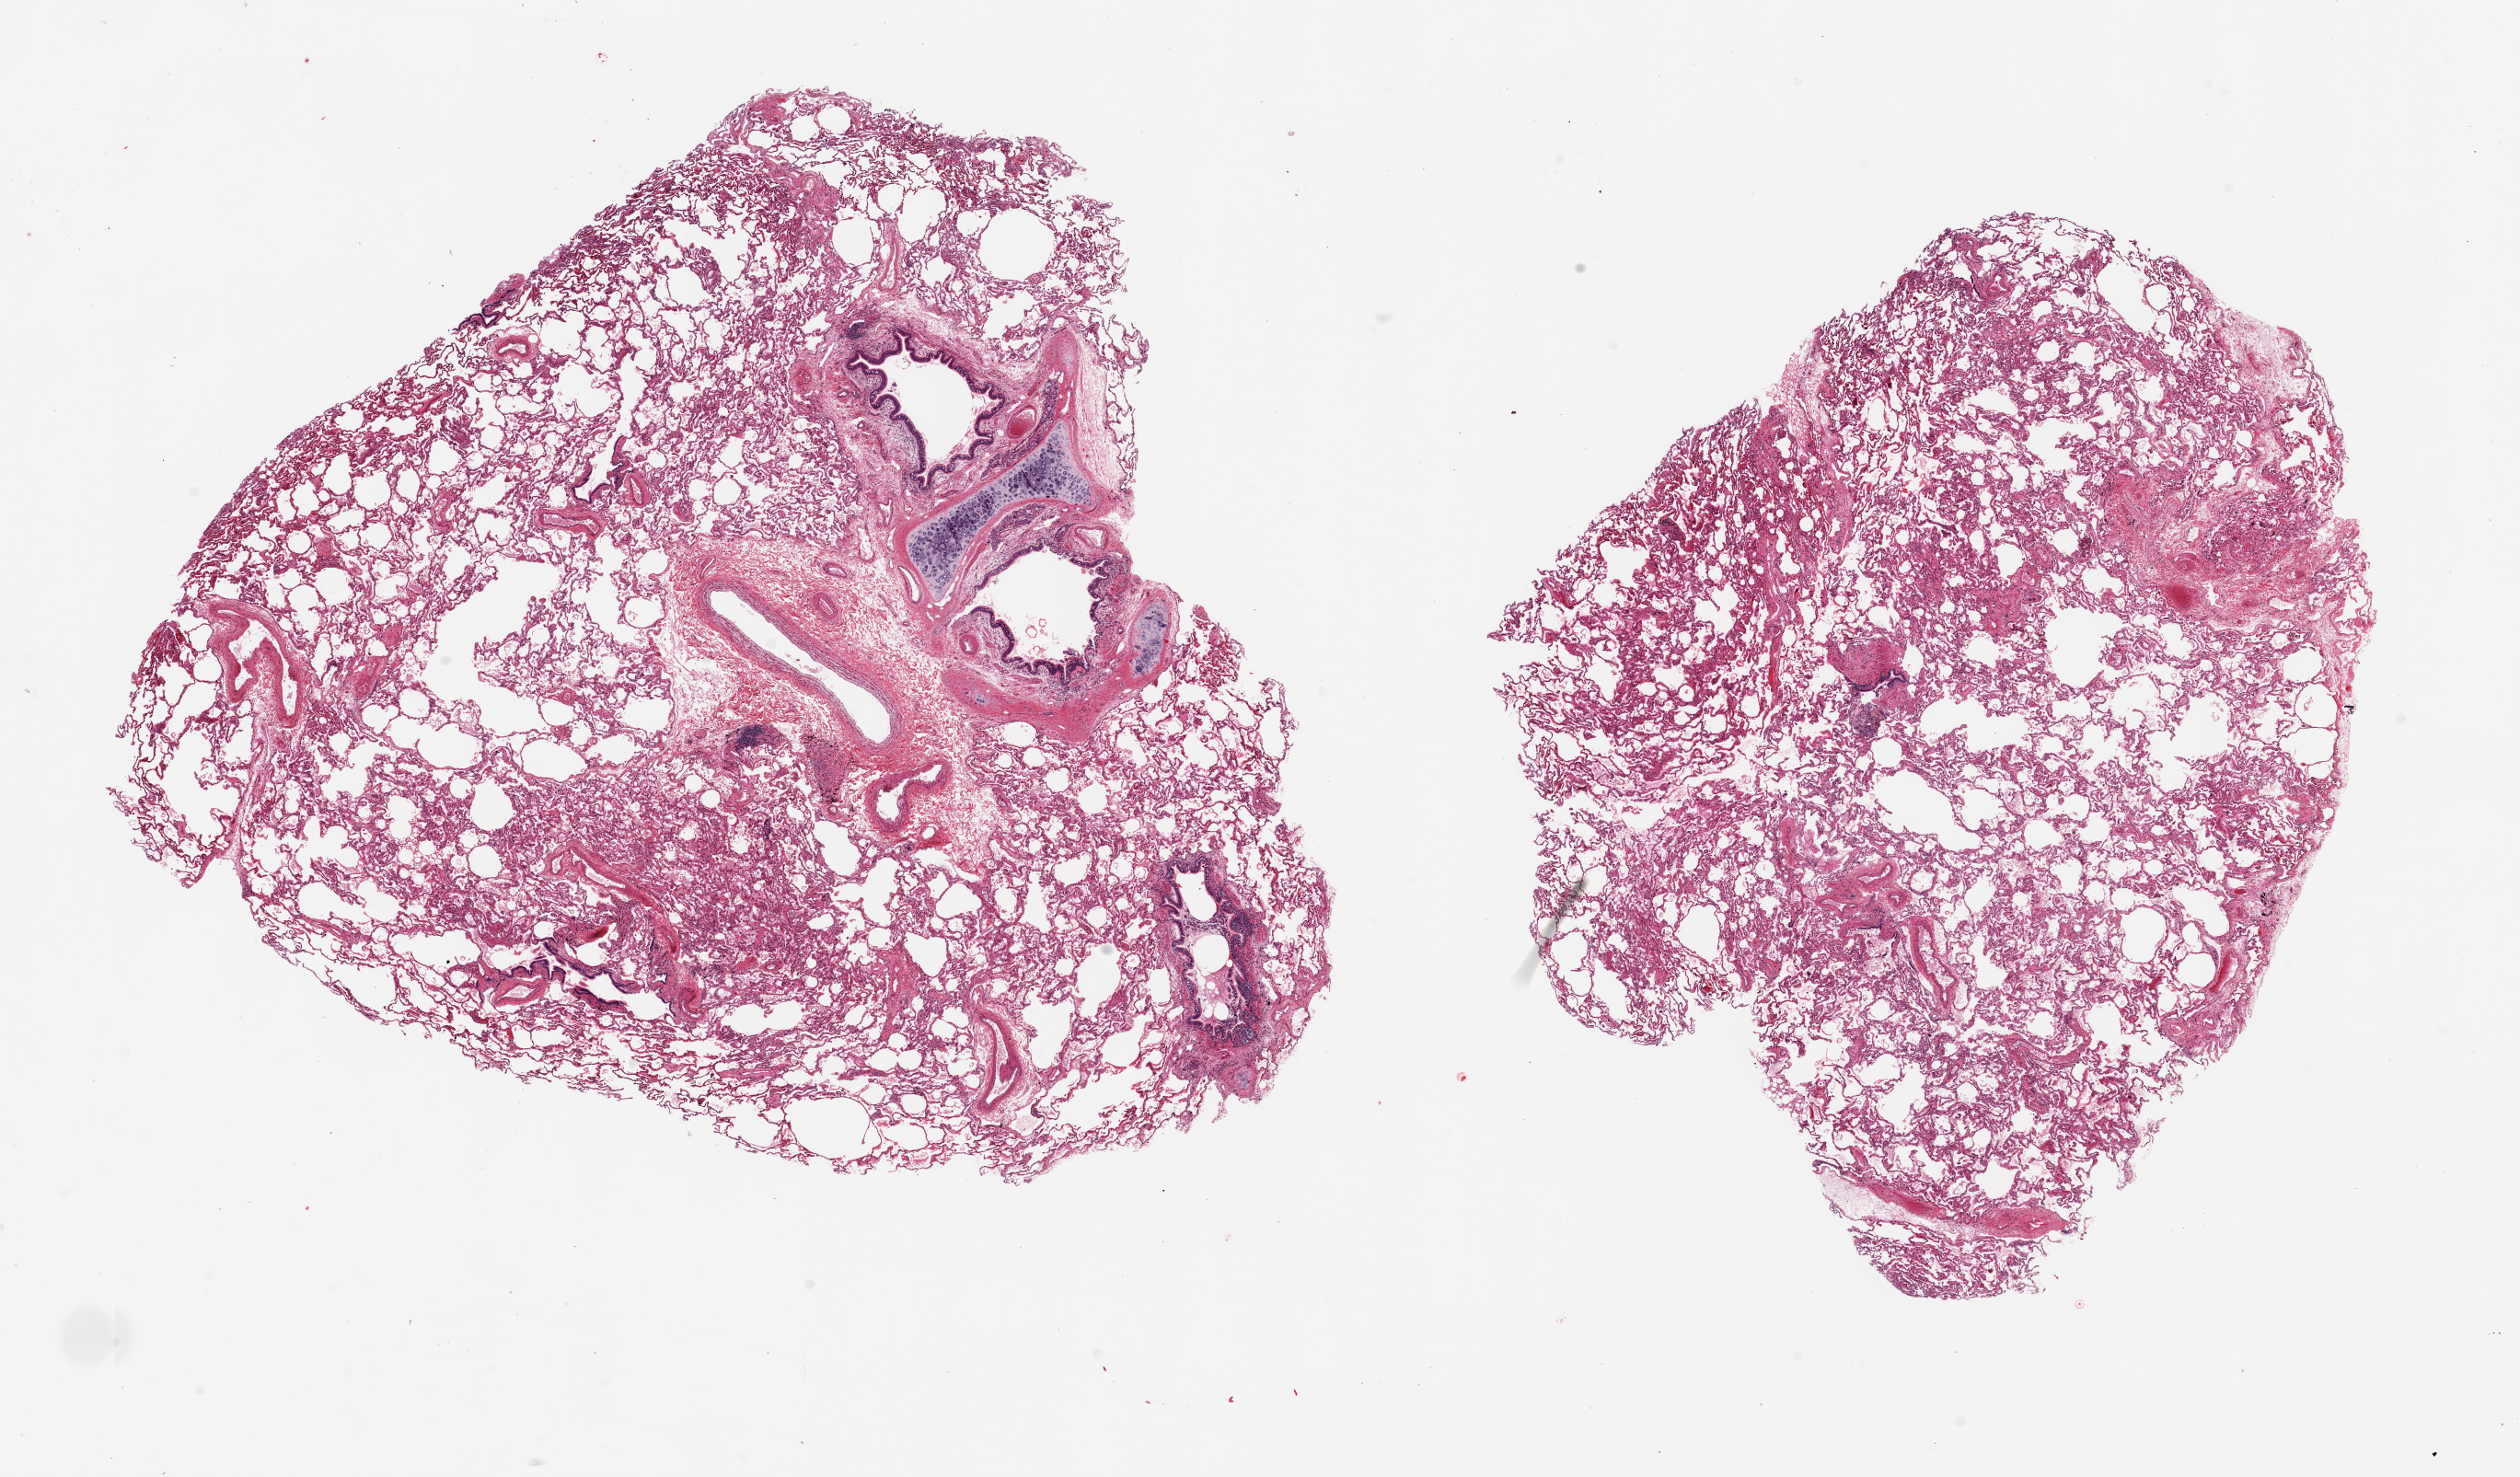
Whole-slide image, haematoxylin and eosin stain, brightfield — shown as a low-resolution overview of the whole scanned area (about 21.7 x 12.7 mm, acquisition: 20x scan); PAXgene-fixed paraffin-embedded (PFPE) section; target tissue: lung; donor tissue sample. Male donor.
Review note (as recorded): 2 ~8.5x8mm aliquots, minimal congestion.